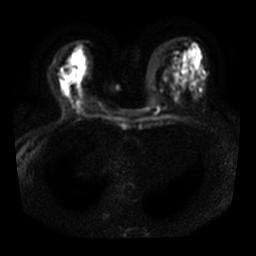
Breast MRI, one axial slice. Slice 14 of 28 in the series (ordered by position). Diffusion-weighted series; image 2 of 4 stored at this slice position (different b-values; order by instance number). 3 T. 5 mm slice thickness. 256 × 256 image matrix, field of view 320 × 320 mm. Female patient.
Annotated regions visible in this slice (manually delineated by an expert):
- tumour on diffusion-weighted imaging: box from (x=60, y=63) to (x=73, y=75) px